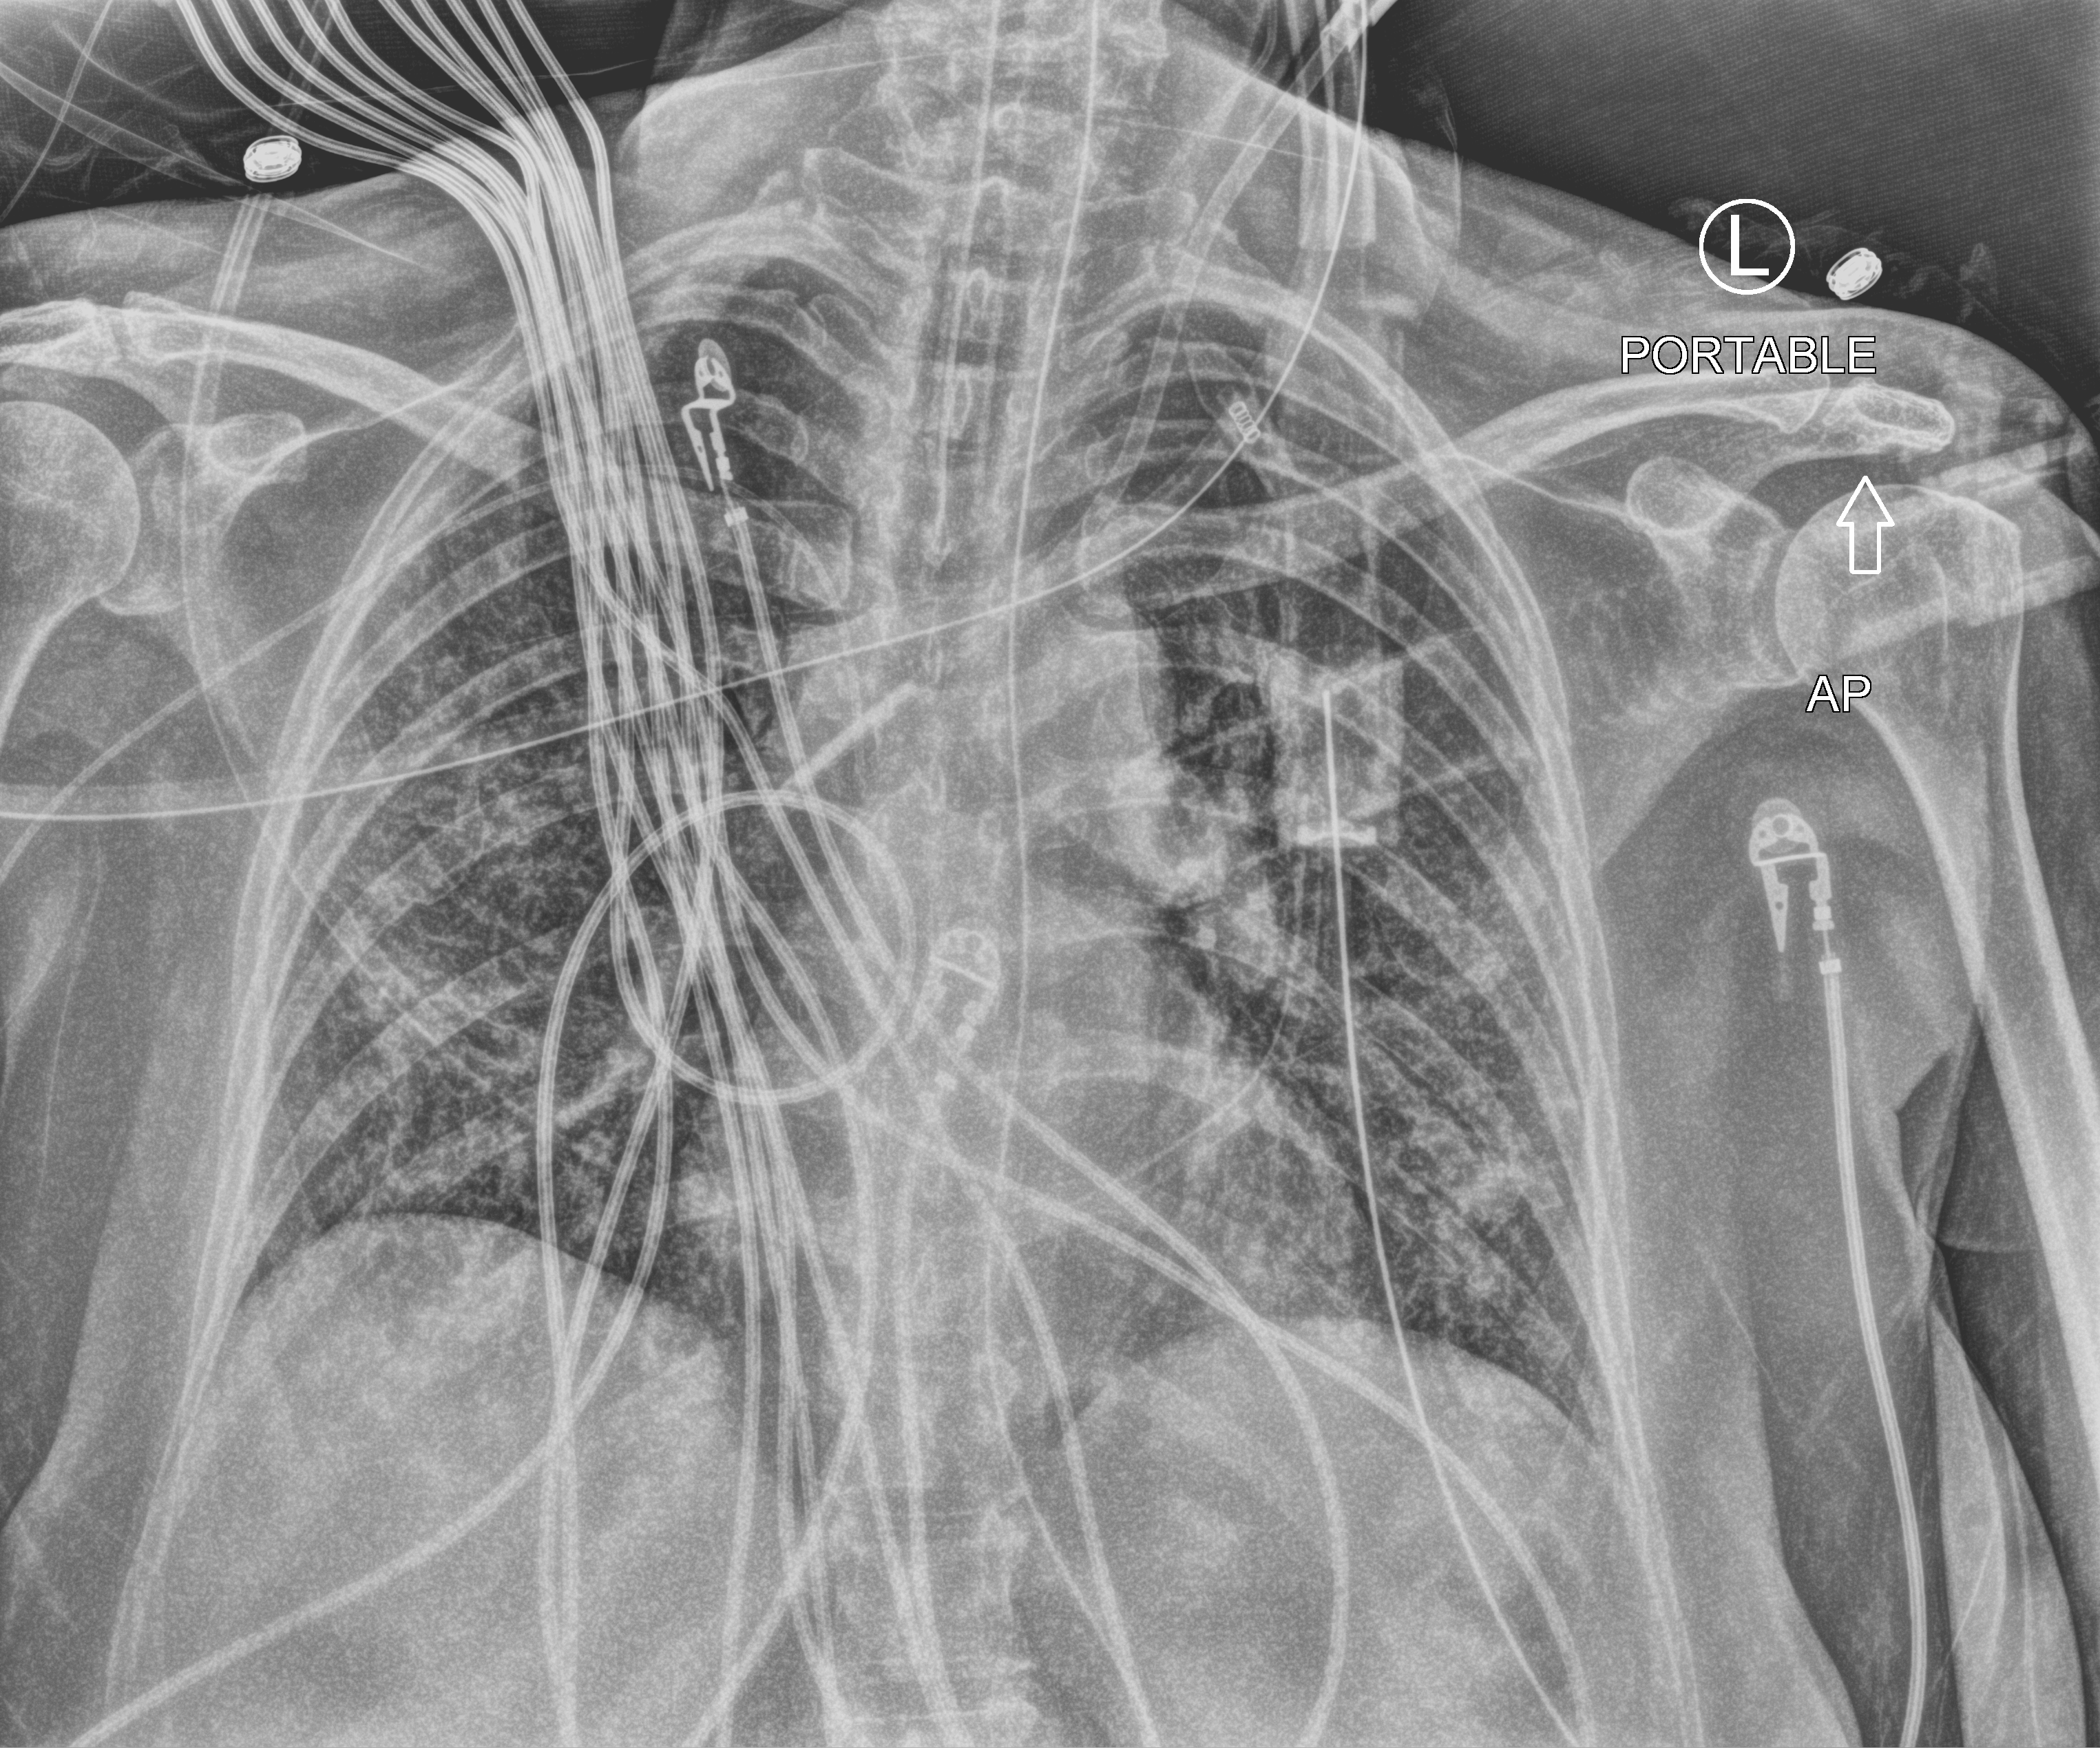
Bedside chest radiograph (computed radiography), anteroposterior (AP) projection. Female patient hospitalised with COVID-19, age 60–74 years.
Hospital-stay facts (about this admission, not read from this image; timing relative to this image not recorded):
- admitted to intensive care during this hospital stay: yes
- length of hospital stay: 43 days
- diabetes (admission record): no